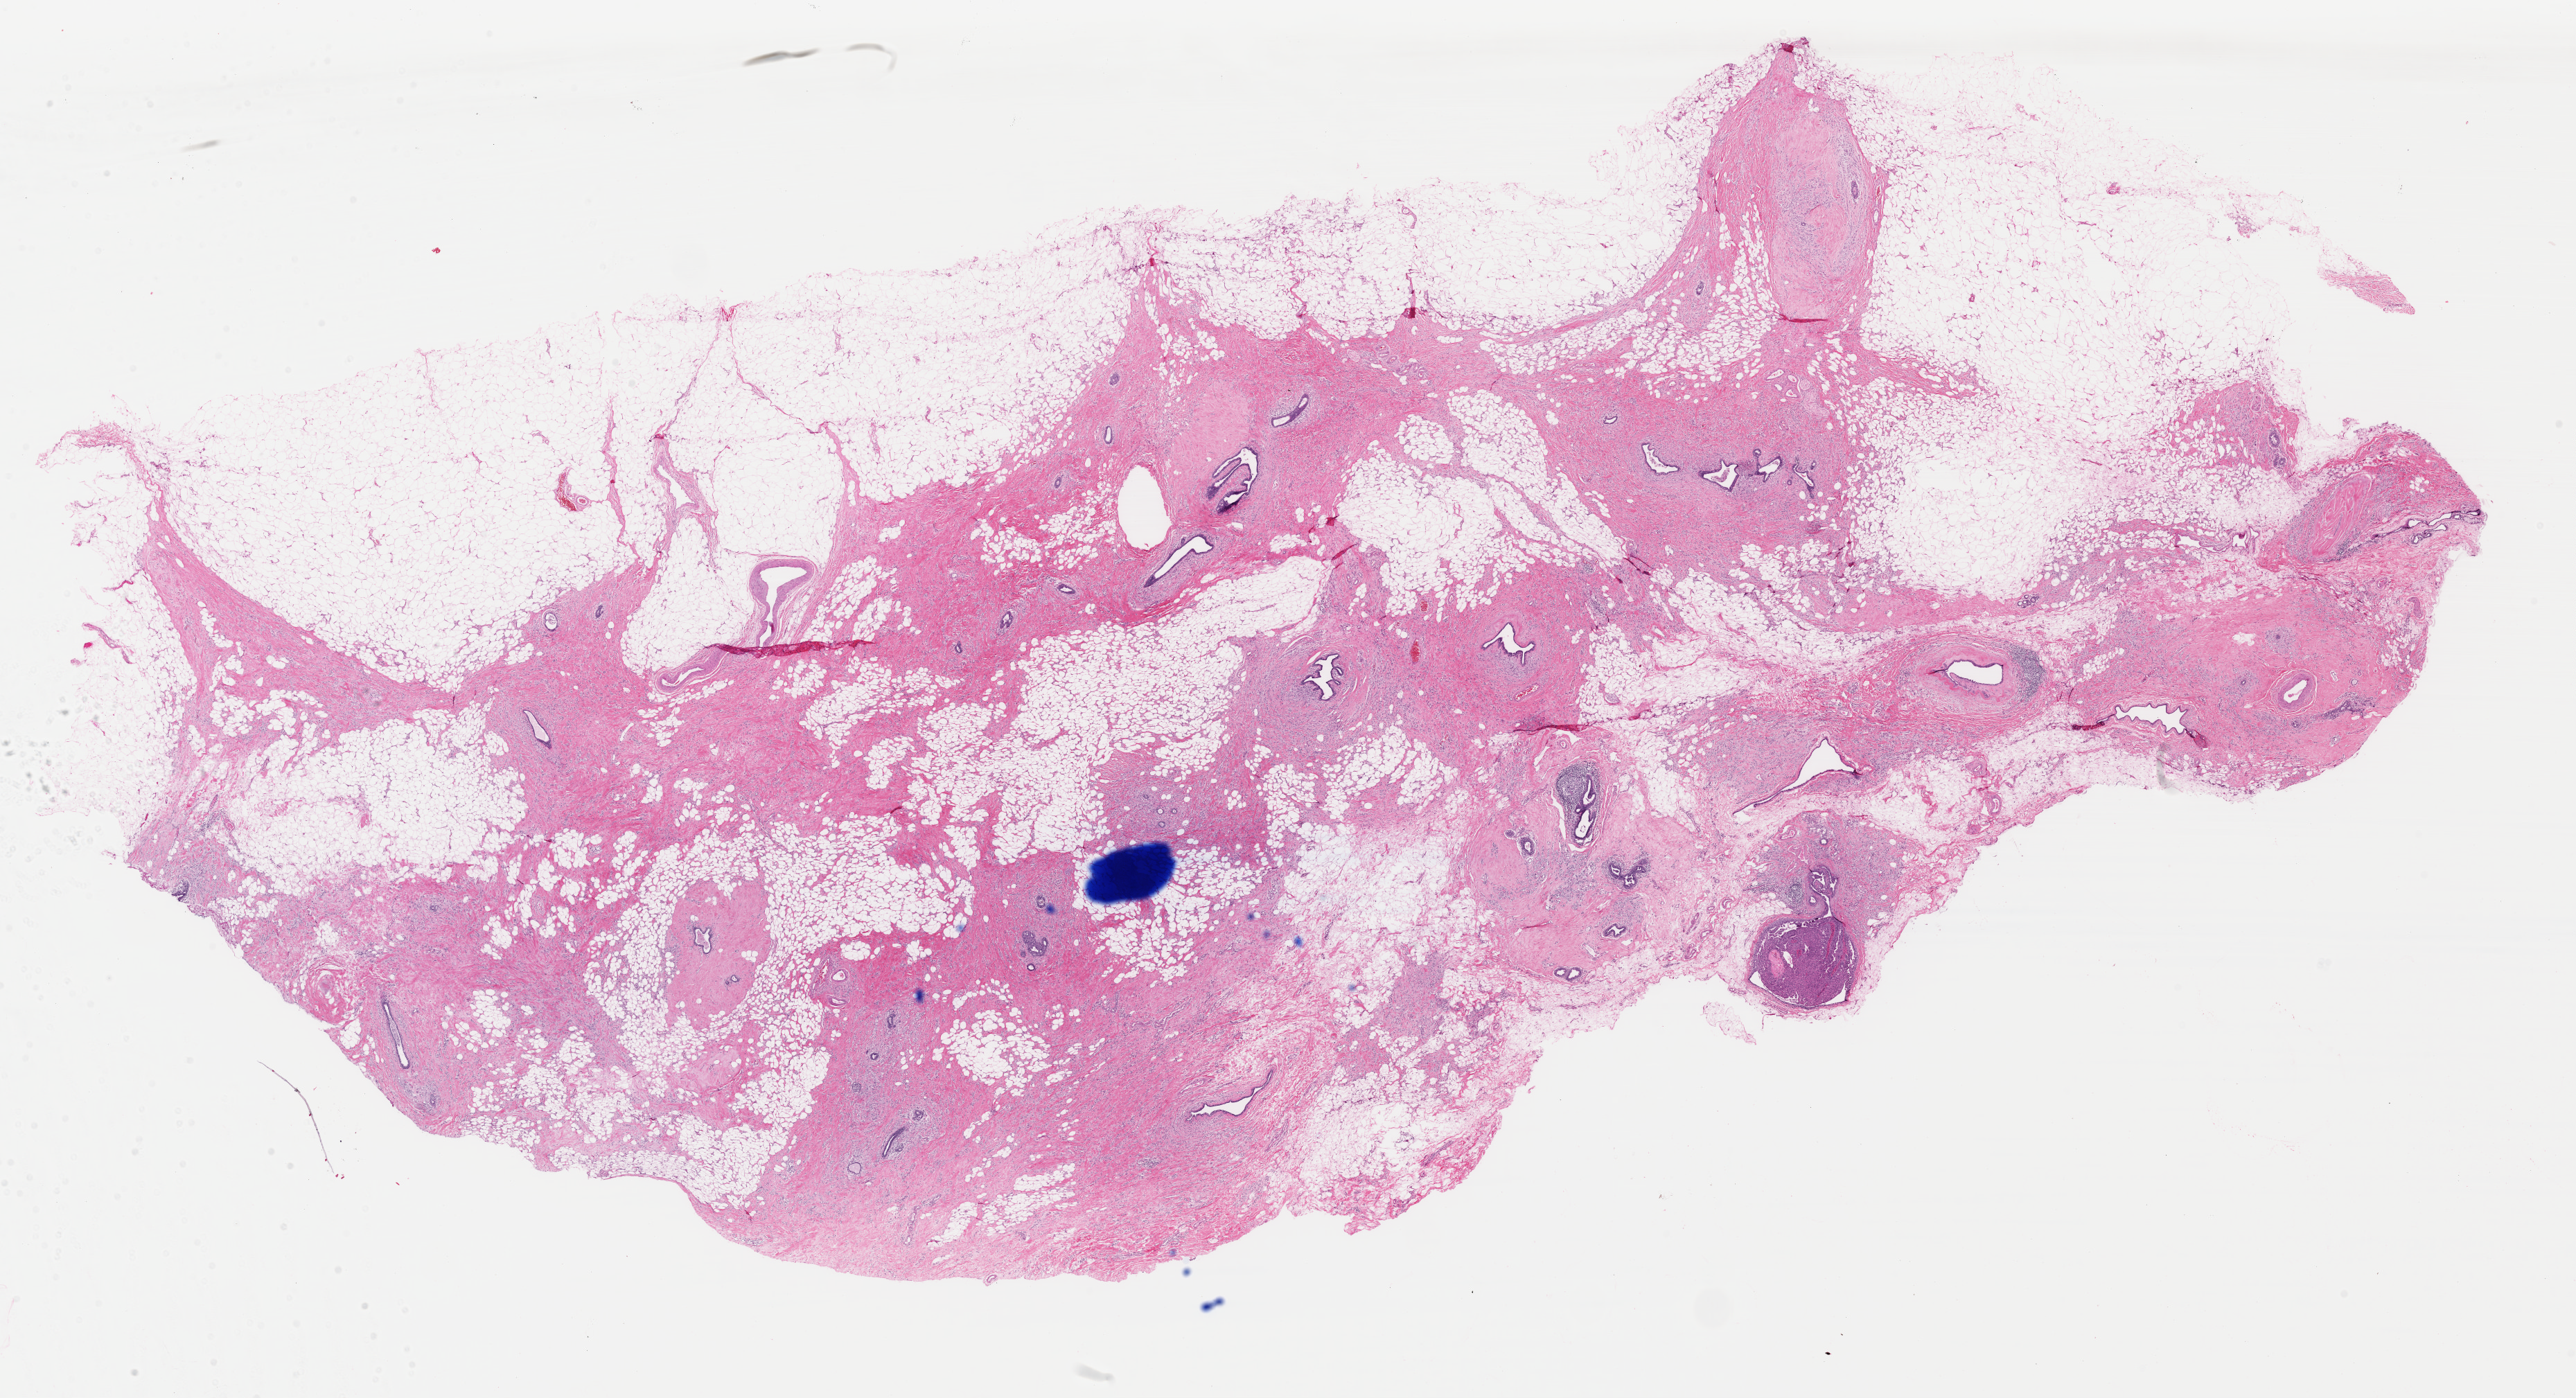
H&E-stained whole-slide image, low-resolution overview of the scanned area, about 29.4 x 15.9 mm (slide scanned at 40x). Formalin-fixed paraffin-embedded (FFPE) diagnostic section. Primary tumour sample from the breast. Patient: female, age at initial diagnosis 68 years.
Histologic diagnosis: Lobular carcinoma, NOS. AJCC pathologic stage: IIB. TNM: T3 N0 (i-) M0.